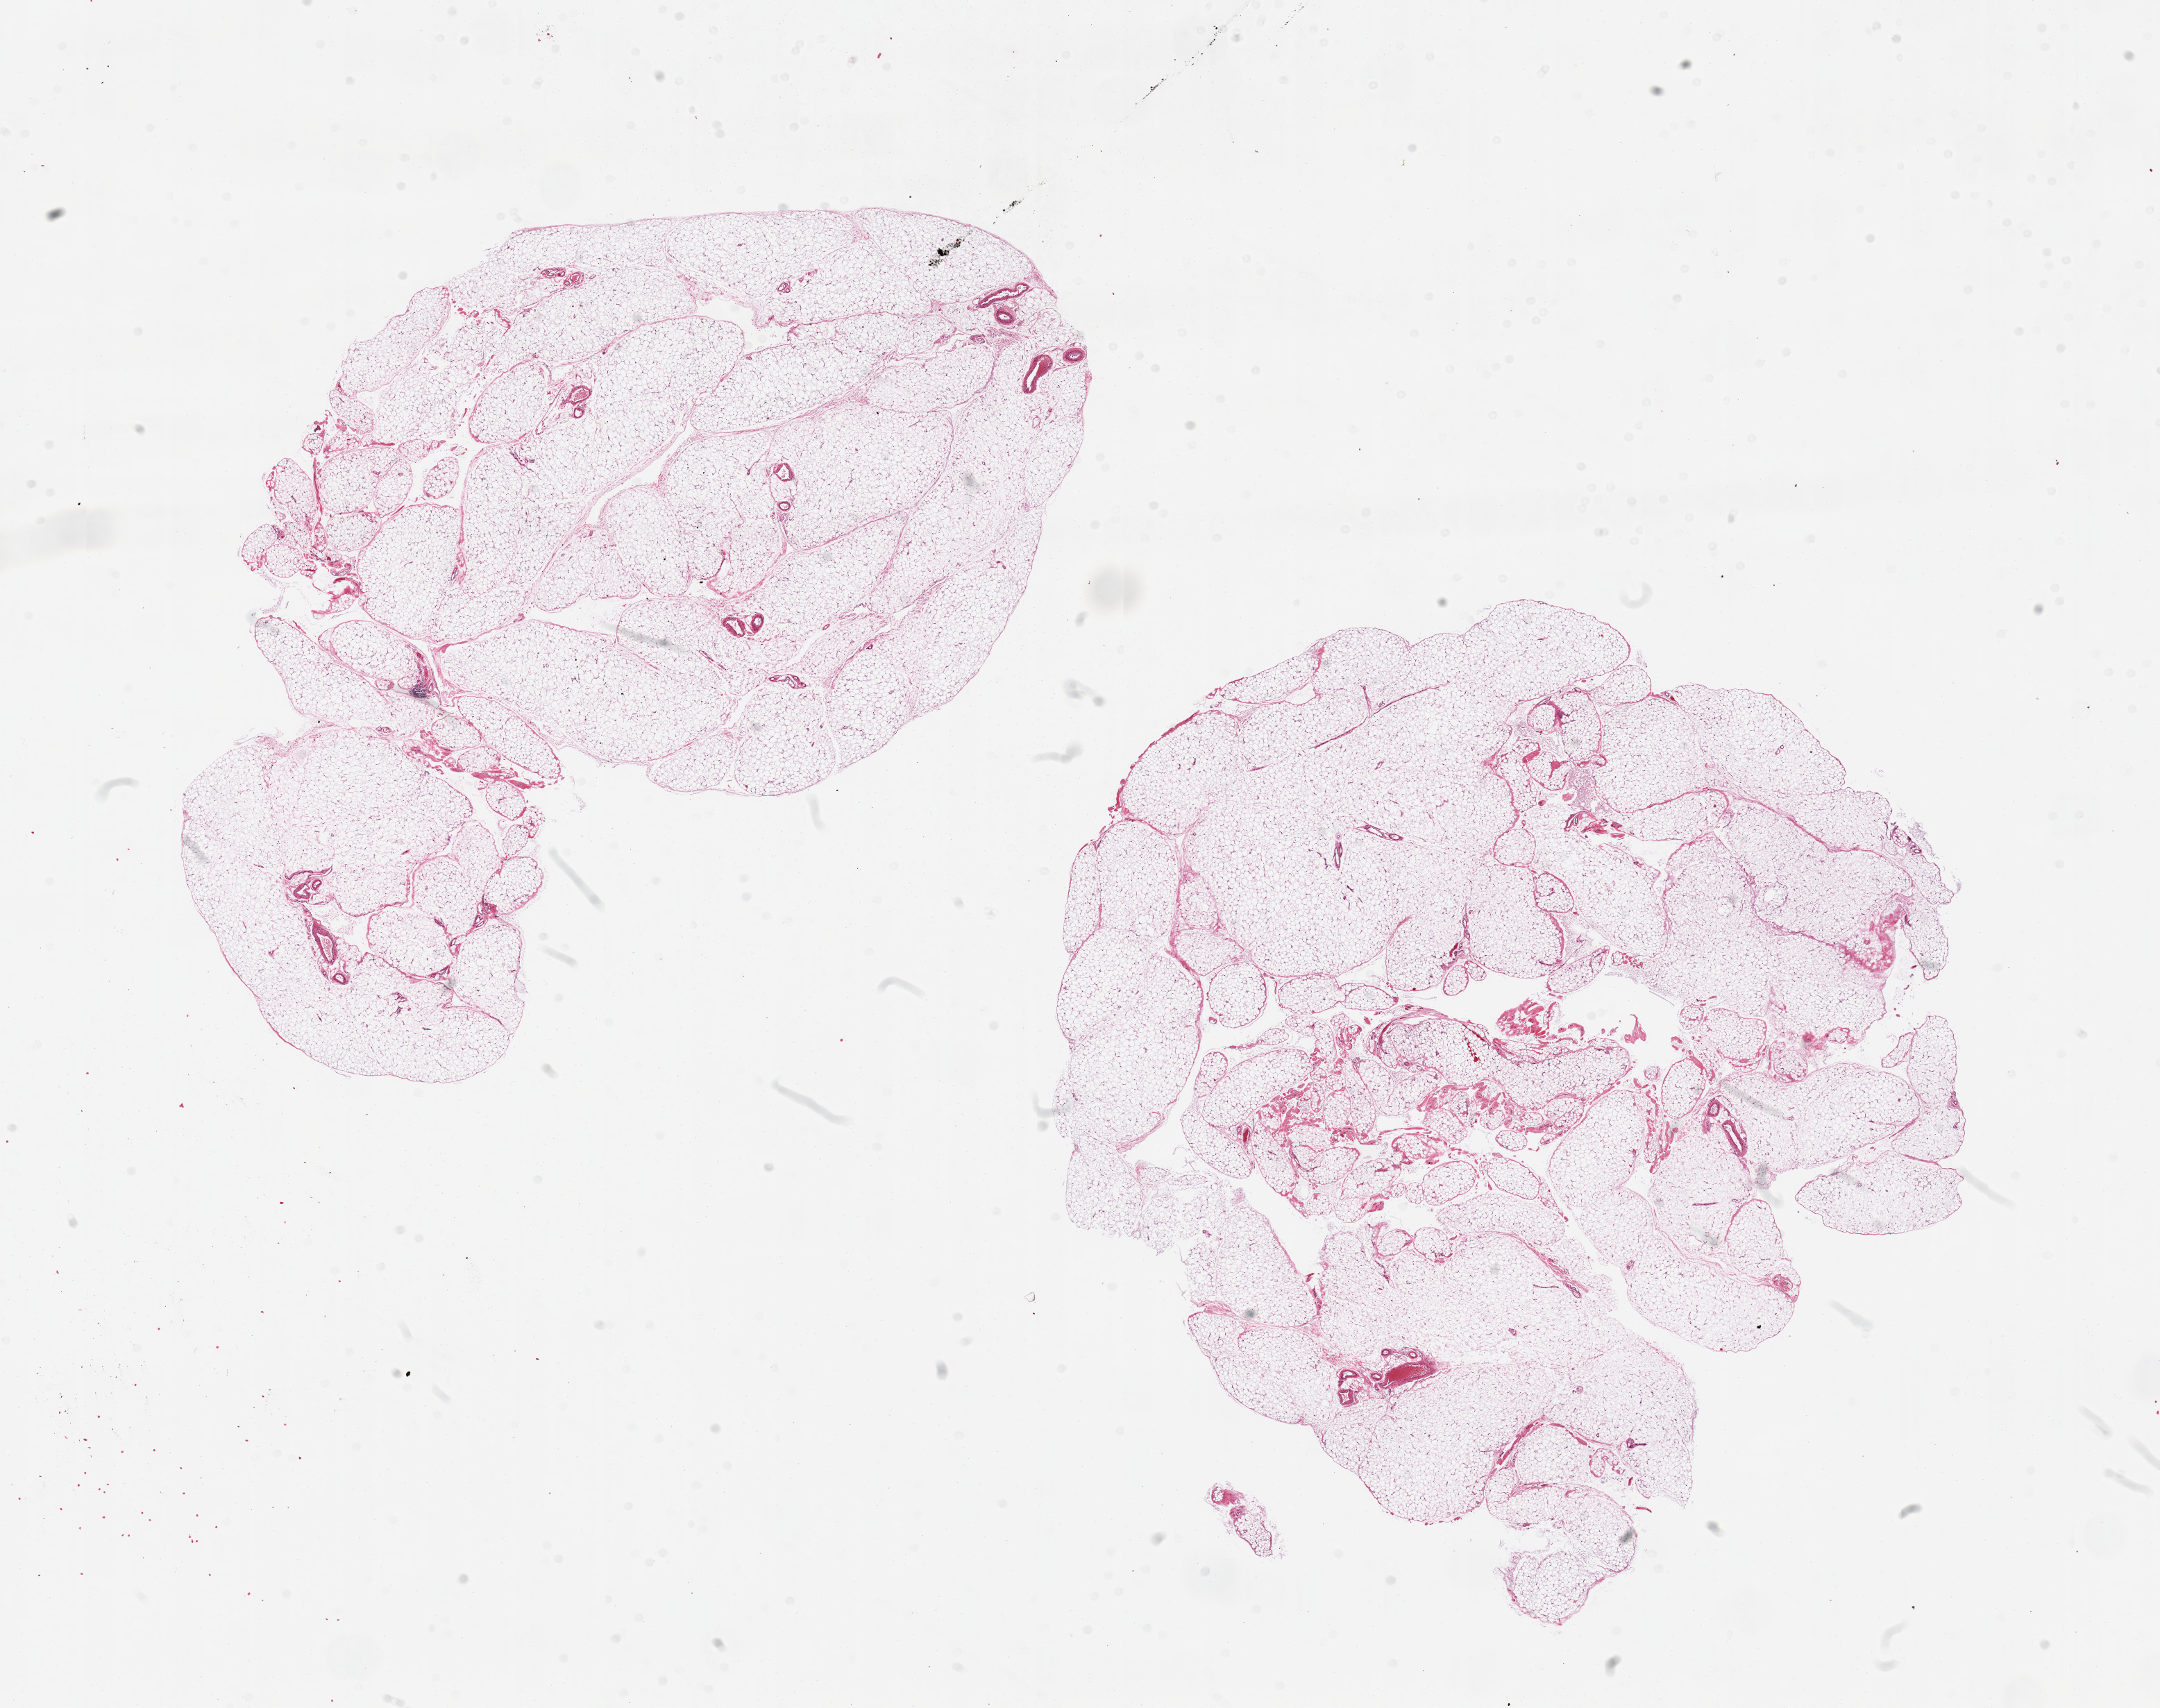
Hematoxylin and eosin (H&E) whole-slide image, brightfield — a low-resolution overview of the entire scanned area, about 24.6 x 19.5 mm; PAXgene-fixed paraffin-embedded (PFPE) section; section of omentum (target tissue); tissue donor sample. Male donor.
Pathologist's review note for this sample: 2 pieces.